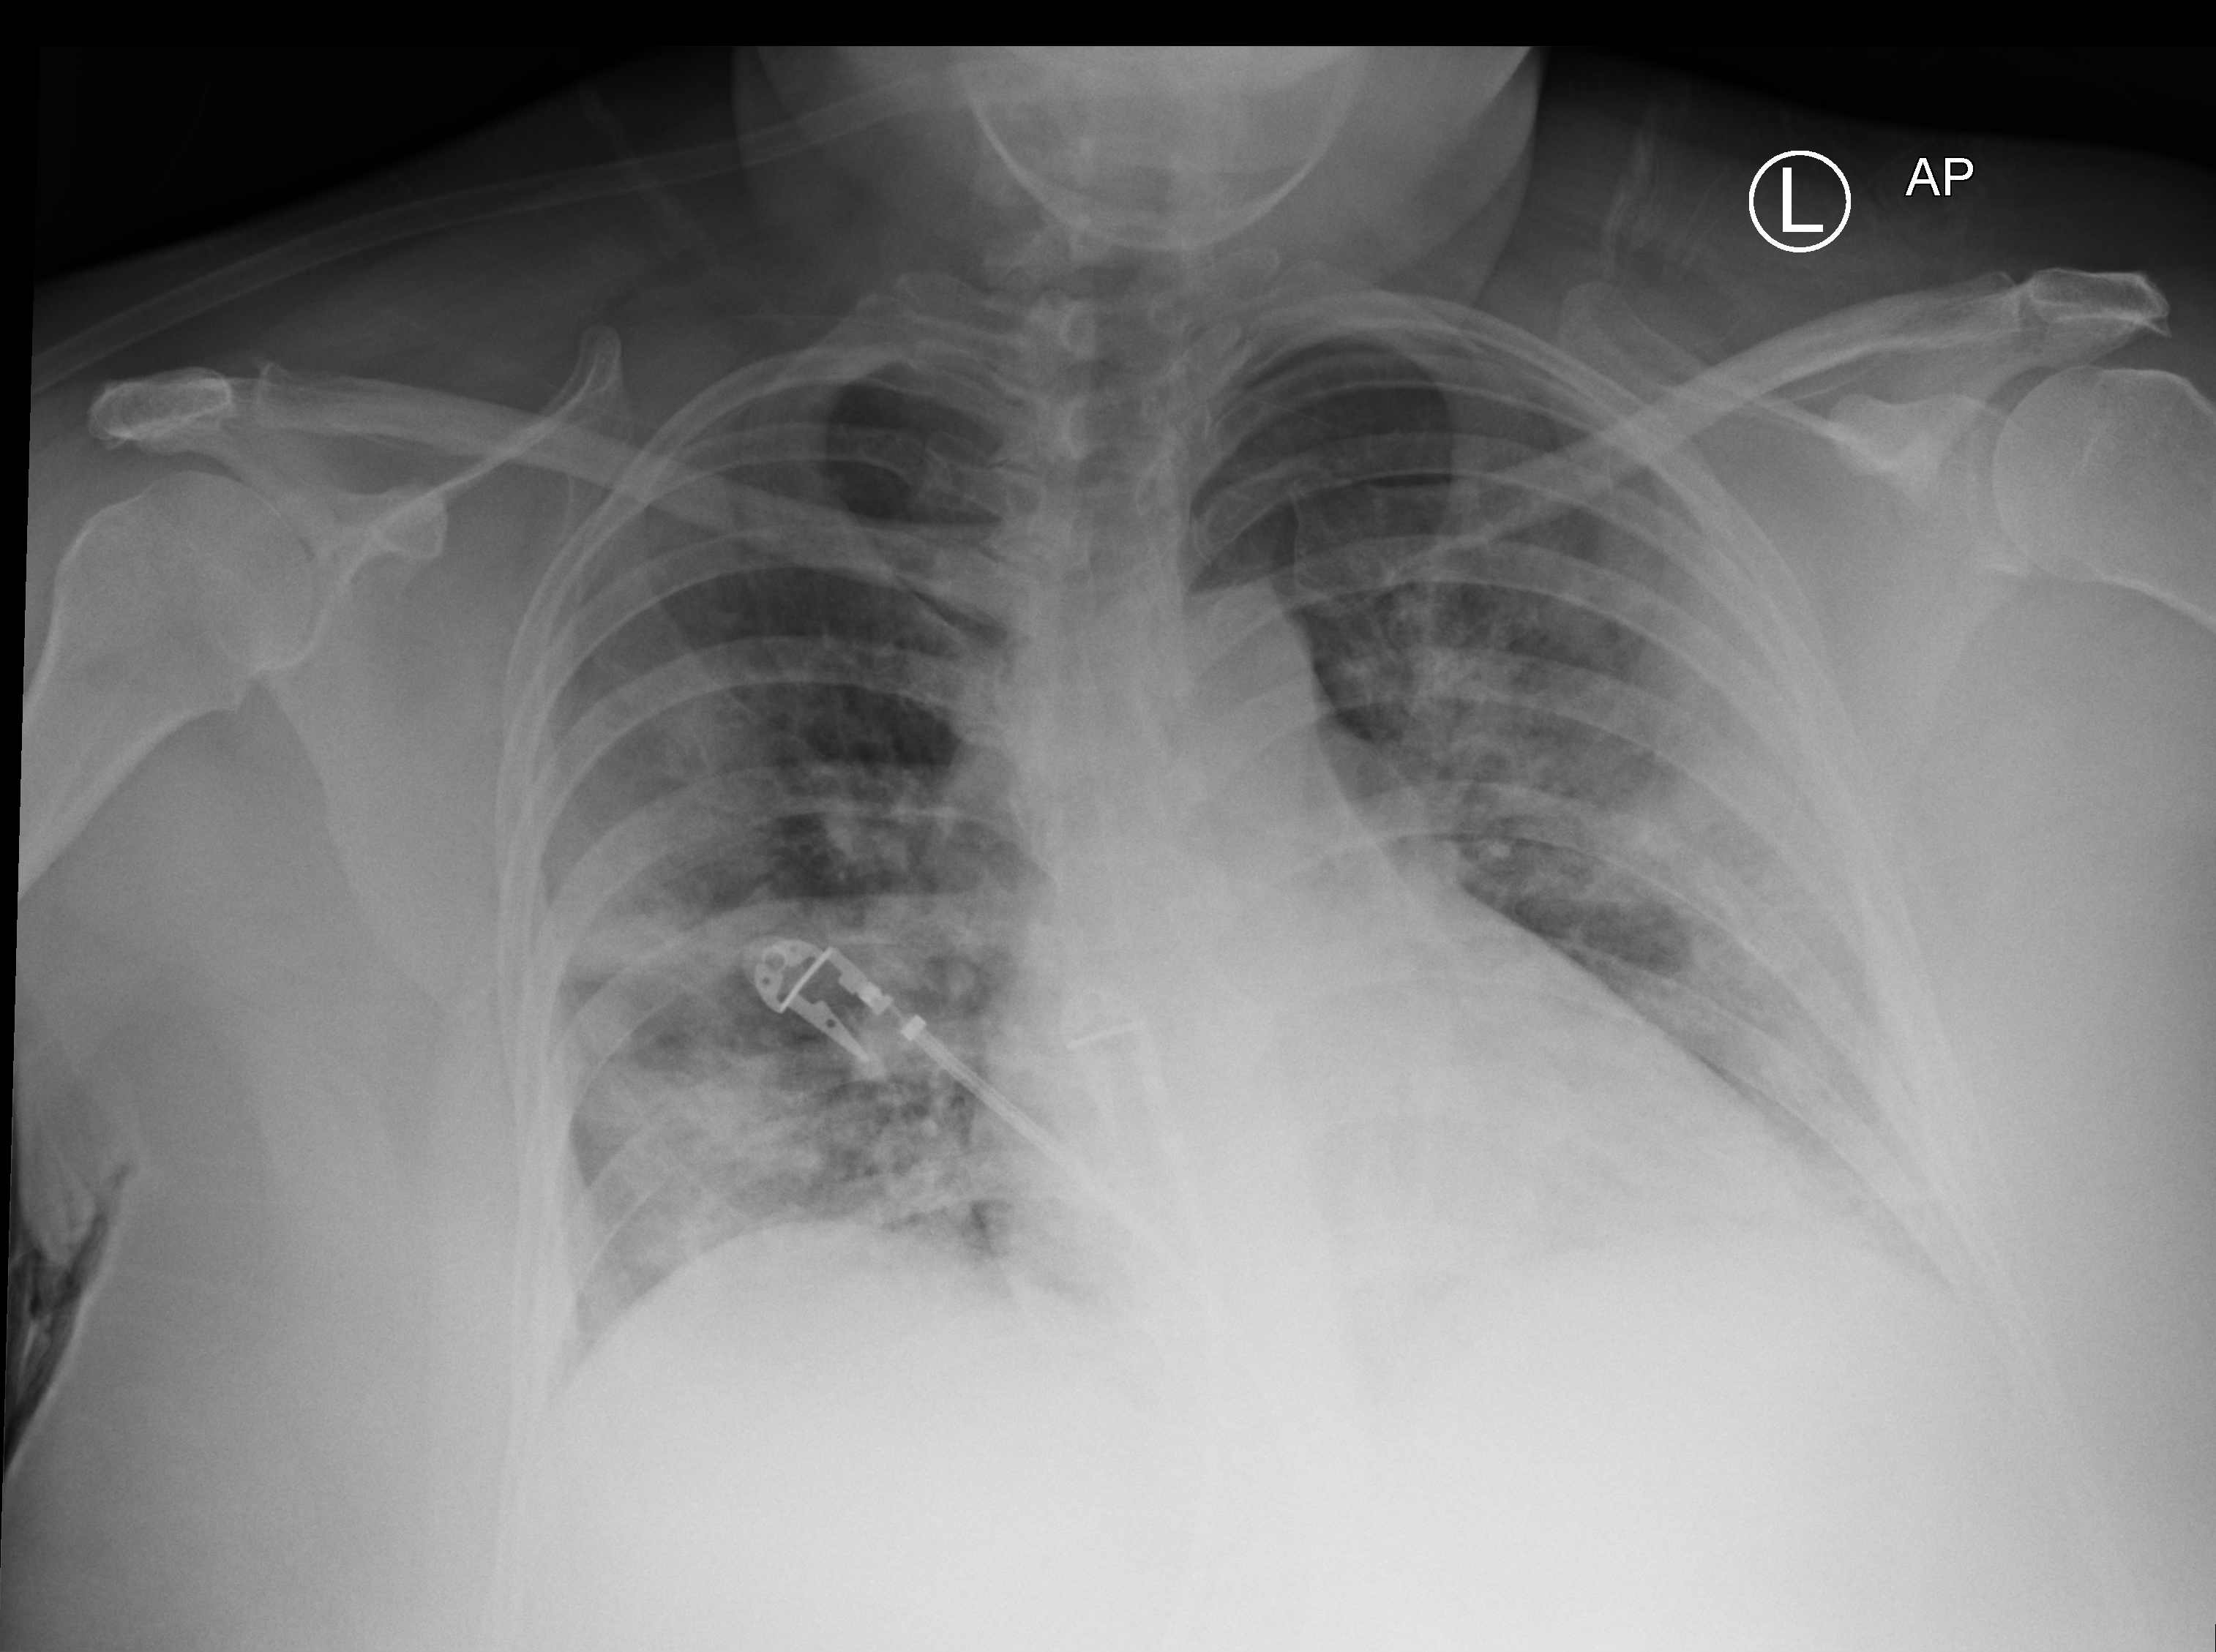
Bedside chest radiograph (computed radiography), anteroposterior (AP) projection. Female patient hospitalised with COVID-19, age 18–59 years.
Hospital-stay facts (about this admission, not read from this image; timing relative to this image not recorded): diabetes (admission record): yes; length of hospital stay: 10 days.